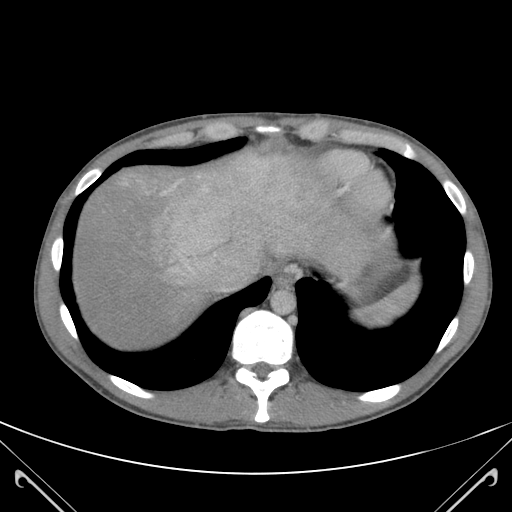
Contrast-enhanced abdominal CT (liver protocol), one axial slice. Position 102 of 118 along the scan axis. 120 kVp. Soft-tissue window (W 400 / L 40 HU). 3 mm slice thickness. 512 × 512 image matrix, field of view 380 × 380 mm. Case-level facts recorded for this patient, not image findings: diagnosis: hepatocellular carcinoma (patient treated with transarterial chemoembolisation; whether this scan precedes or follows treatment is not stated here); TNM stage (as recorded): Stage-IIIB; Child-Pugh class: A; tumour nodularity: uninodular.
Annotated regions visible in this slice (semi-automatic segmentation, software-assisted and operator-edited):
- abdominal aorta: box from (x=272, y=289) to (x=294, y=313) px
- liver parenchyma outside the tumour (the mass and vessels are separate outlines, so this box may not span the whole liver): (x=75, y=153)–(x=317, y=349)
- mass: (x=141, y=164)–(x=286, y=272)
- liver vessels: (x=170, y=157)–(x=298, y=291)